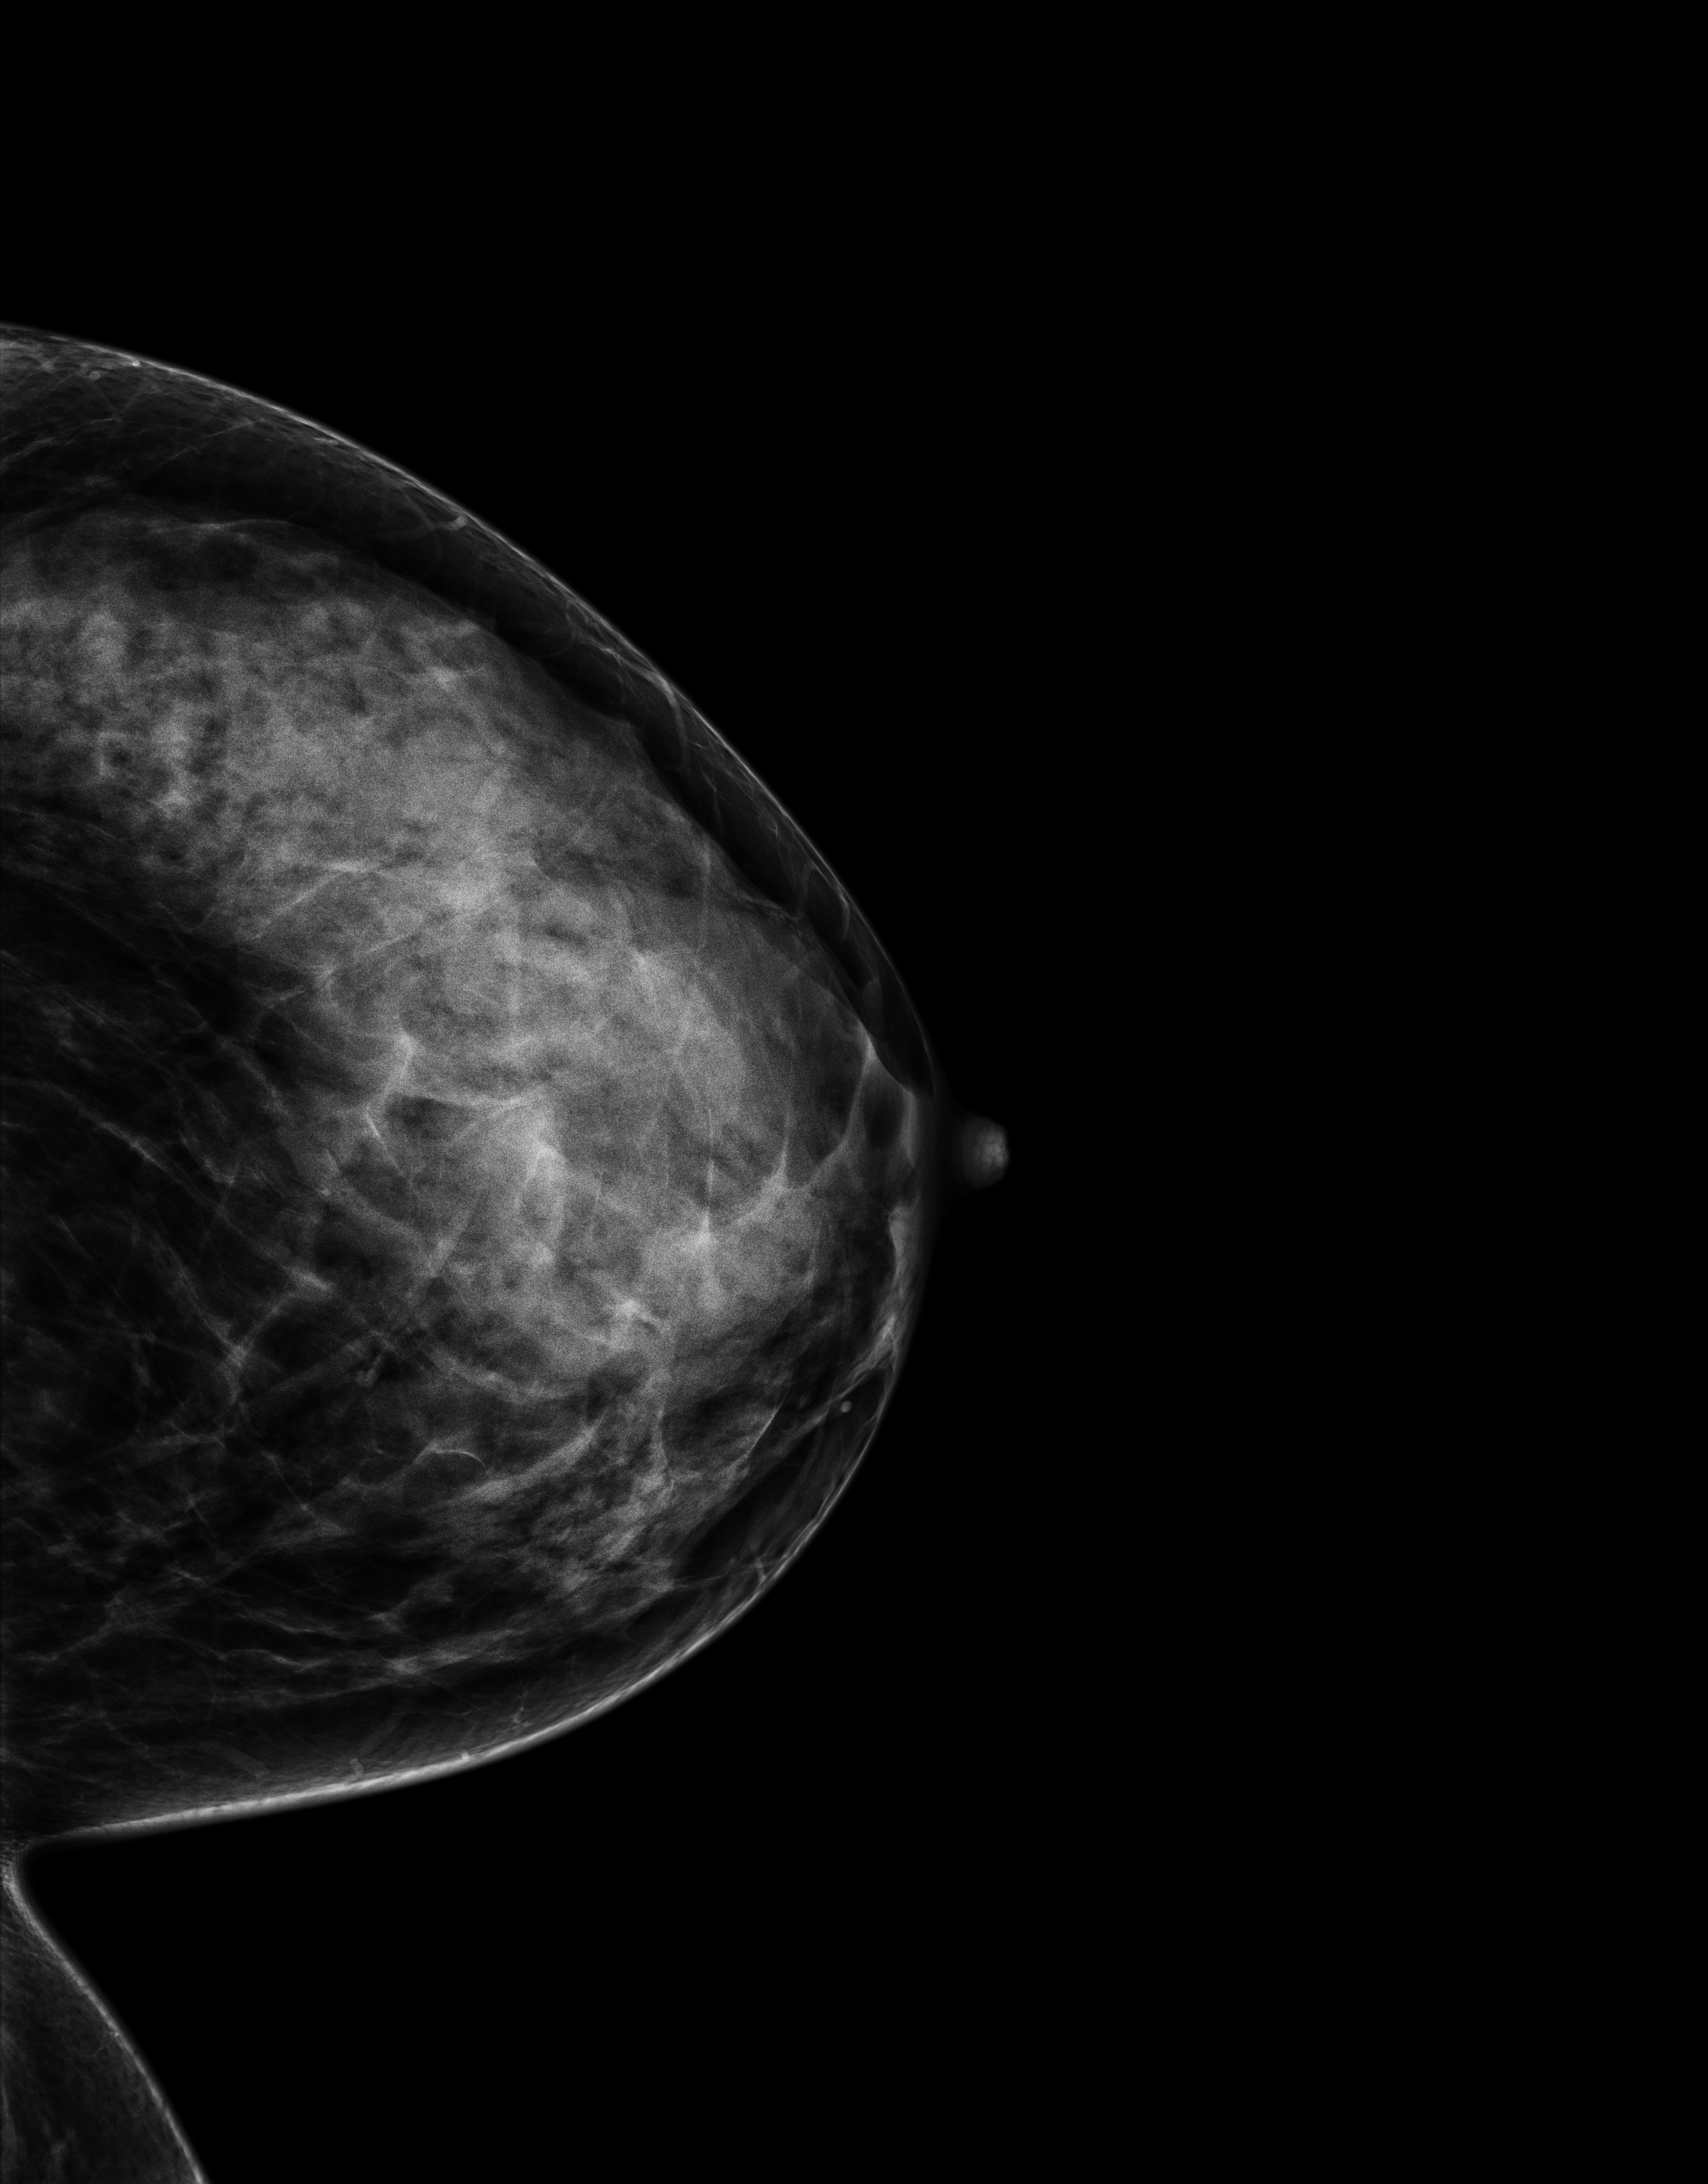
Digital mammogram (FFDM), left breast, CC view, annual screening mammography examination, compressed breast thickness 62 mm. Patient aged 43 years (female).
Breast density at the screening exam (both breasts): extremely dense (BI-RADS density category d). Final BI-RADS category for the screening round (tomosynthesis exam, both breasts): category 1. Recall: no recall after this screen.